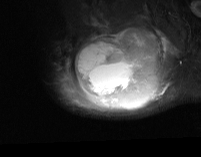
MRI of an extremity soft-tissue mass, one axial slice; position 52 of 74 along the scan axis; STIR; MR volume resampled by the dataset authors to the PET/CT grid (not the native acquisition matrix); 3.27 mm slice thickness; 201 × 157 image matrix, field of view 196 × 153 mm. Male patient. Case-level facts recorded for this patient, not image findings: histological type: pleiomorphic spindle cell undifferentiated; grade: high; site of the primary tumour: right parascapusular.
Annotated regions visible in this slice (expert contour drawn on MRI and transferred to this co-registered scan by the dataset authors):
- gross tumour volume including surrounding oedema: bounding box <56,29,175,111> (left, top, right, bottom; pixels)
- gross tumour volume (mass): <76,34,157,110>